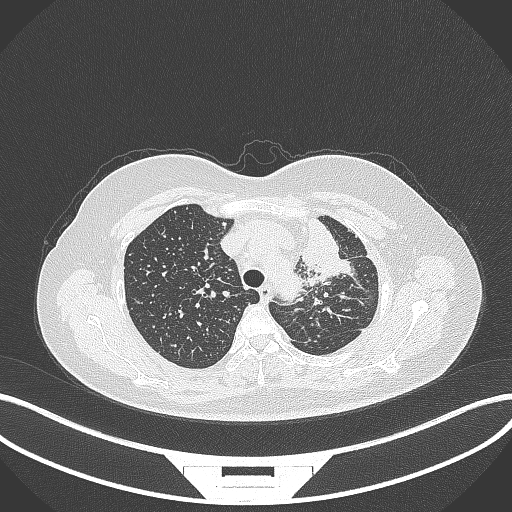
Chest CT, one axial slice; position 259 of 348 along the scan axis; lung window (W 1500 / L -600 HU); 1 mm slice thickness; 512 × 512 image matrix, field of view 400 × 400 mm. Patient: female, 49 years. From the clinical record (not read from this slice): clinical TNM (as recorded): T1c N0 M1.
Annotated regions visible in this slice (rectangle marked by the reading radiologist):
- lung tumour (recorded histology: adenocarcinoma): box from (x=294, y=215) to (x=355, y=286) px